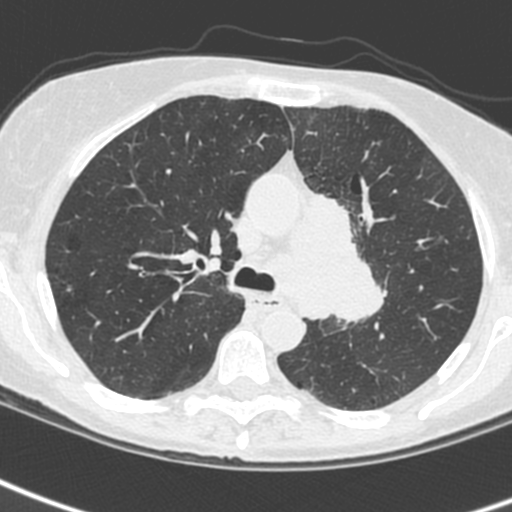
Low-dose screening chest CT, one axial slice; position 164 of 242 along the scan axis; lung window (W 1500 / L -600 HU); 1.3 mm slice thickness; 512 × 512 image matrix, field of view 284 × 284 mm.
Structures marked on this image (manually delineated by an expert):
- lesion 3 (tumor, upper lobe of left lung): bounding box (x1, y1, x2, y2) in pixels: (307, 193, 385, 323)